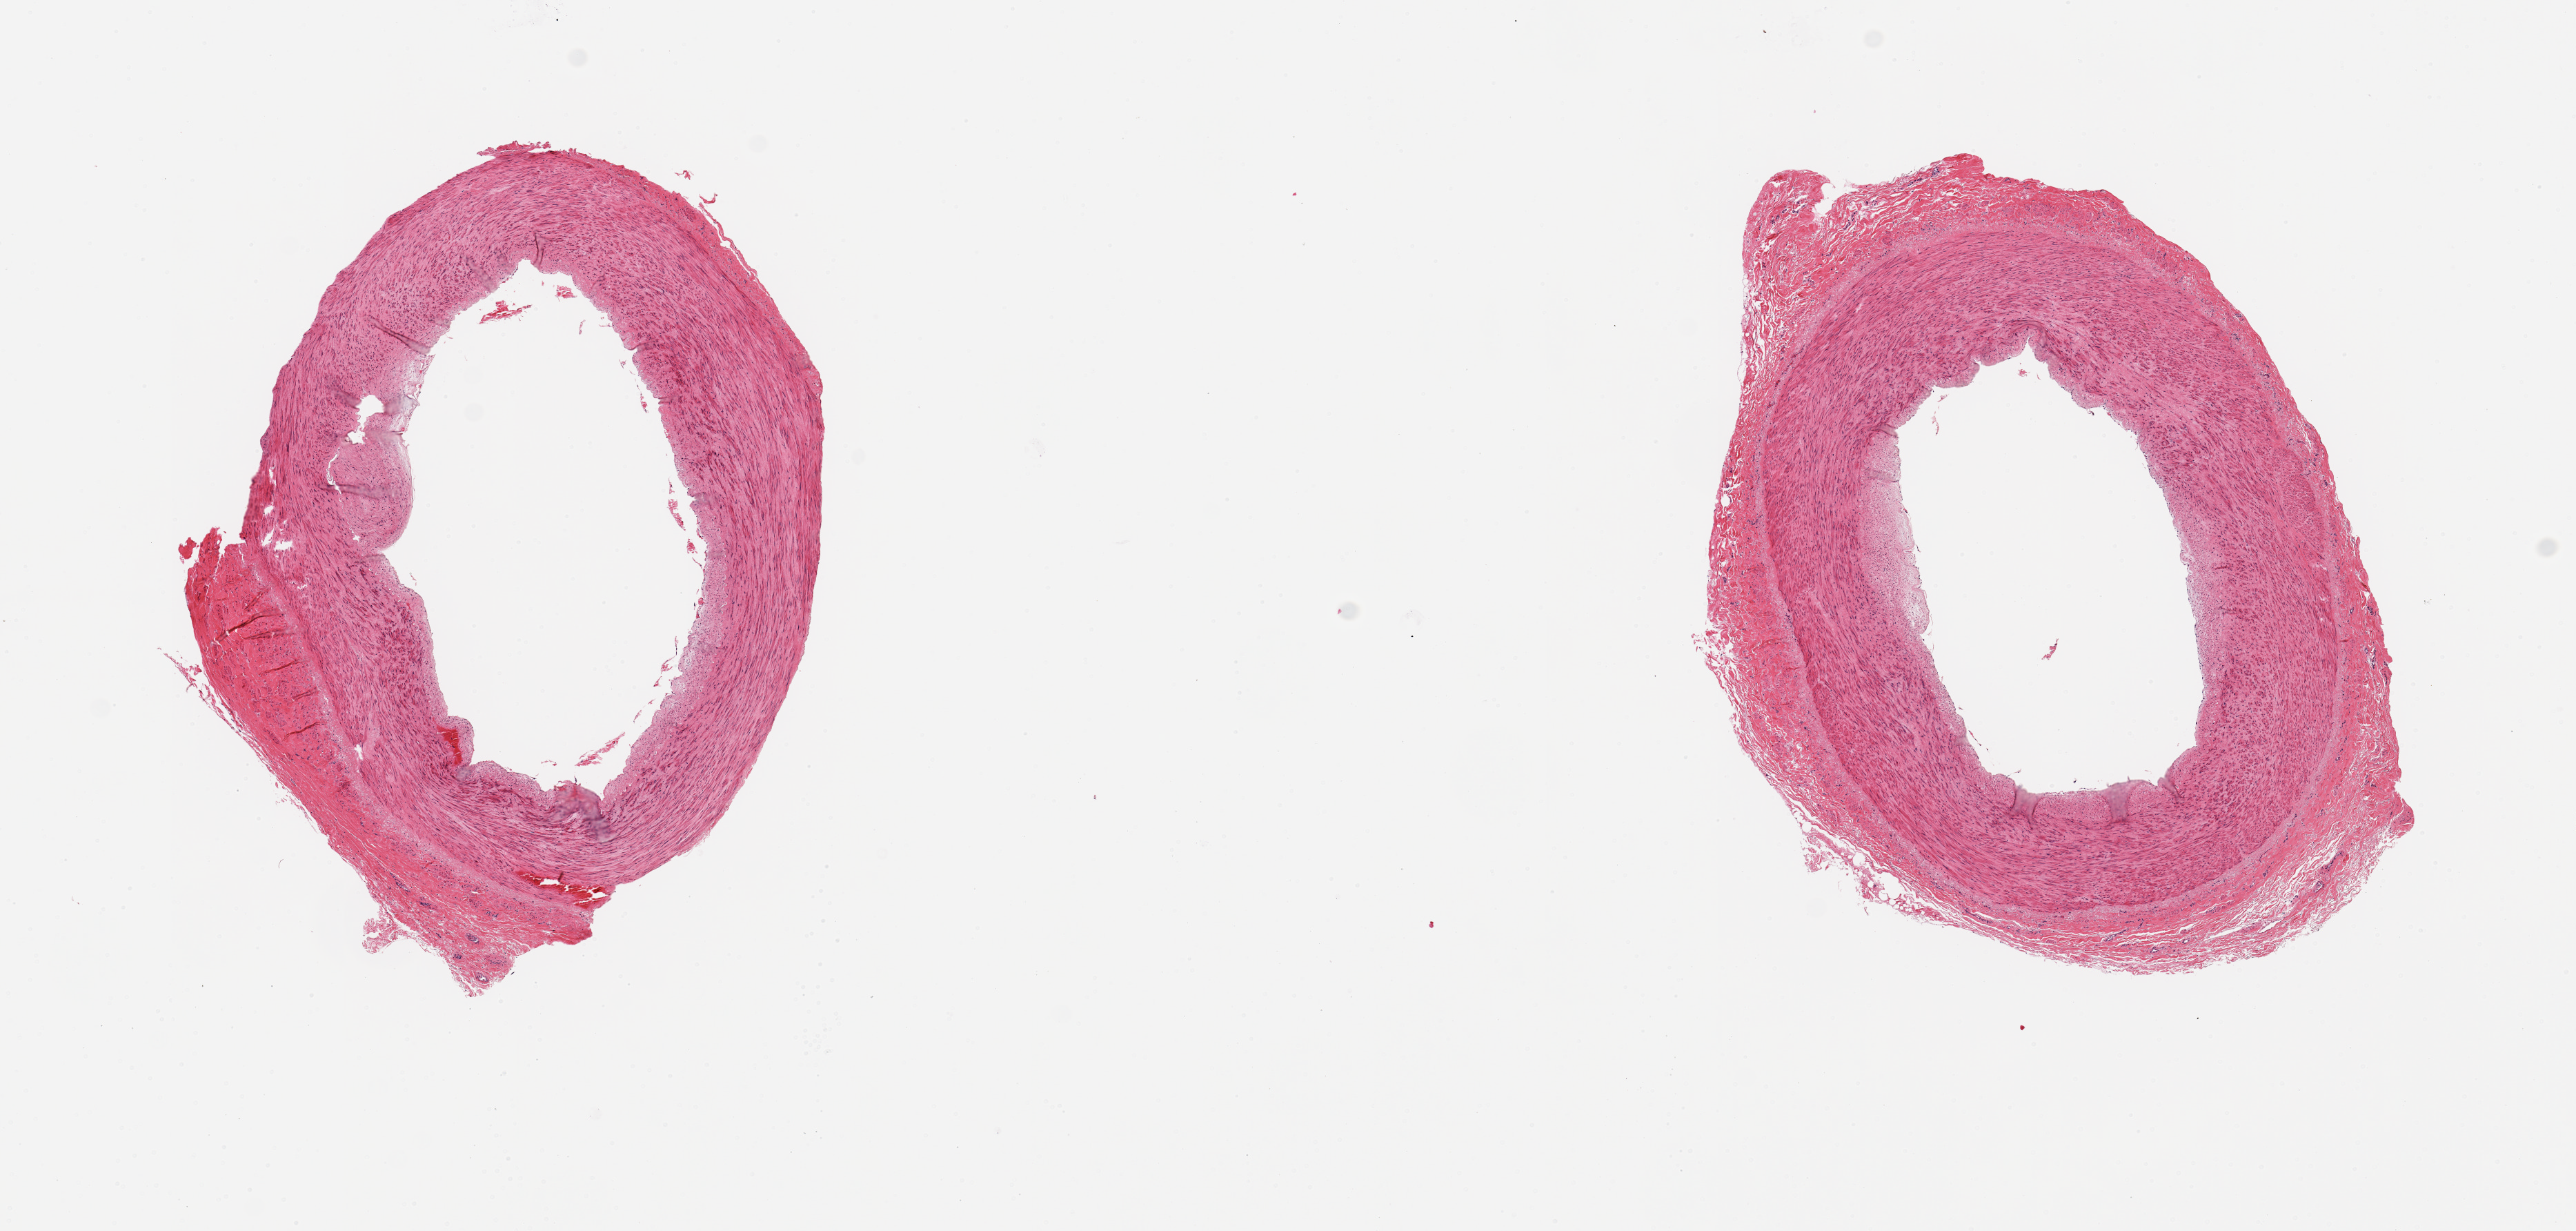
Whole-slide image, hematoxylin and eosin (H&E) stain, a low-resolution overview of the entire scanned area, about 14.8 x 7.1 mm. PAXgene-fixed paraffin-embedded (PFPE) section. Sampled site (target tissue): tibial artery. Tissue donor sample. Male donor.
Pathologist's review note for this sample: 2 pieces; well trimmed.